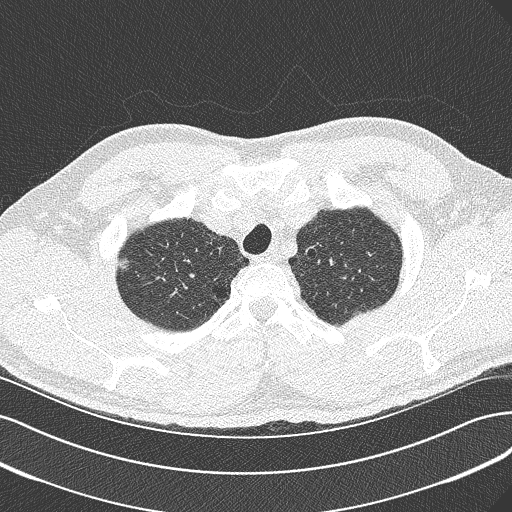
Low-dose screening chest CT, axial slice. Baseline annual screen. Lung window (W 1500 / L -600 HU). Lung (sharp) reconstruction kernel (B50f). 512 × 512 image matrix, field of view 360 × 360 mm. Male, age 56 years at enrolment. Current smoker at enrolment.
Lesion marked by an expert reader, bounding box [x1, y1, x2, y2] px = [105, 248, 146, 287]. Screening reader's record for this exam (one nodule recorded; not confirmed to be the boxed lesion): non-calcified nodule or mass ≥4 mm, right upper lobe, 10 × 7 mm, spiculated (stellate) margins, soft tissue attenuation. Participant outcome: lung cancer diagnosed 517 days after this screen — bronchiolo-alveolar carcinoma, non-mucinous, right upper lobe, moderately differentiated (G2), stage IIIB (AJCC 6th edition), 10 mm at pathology.